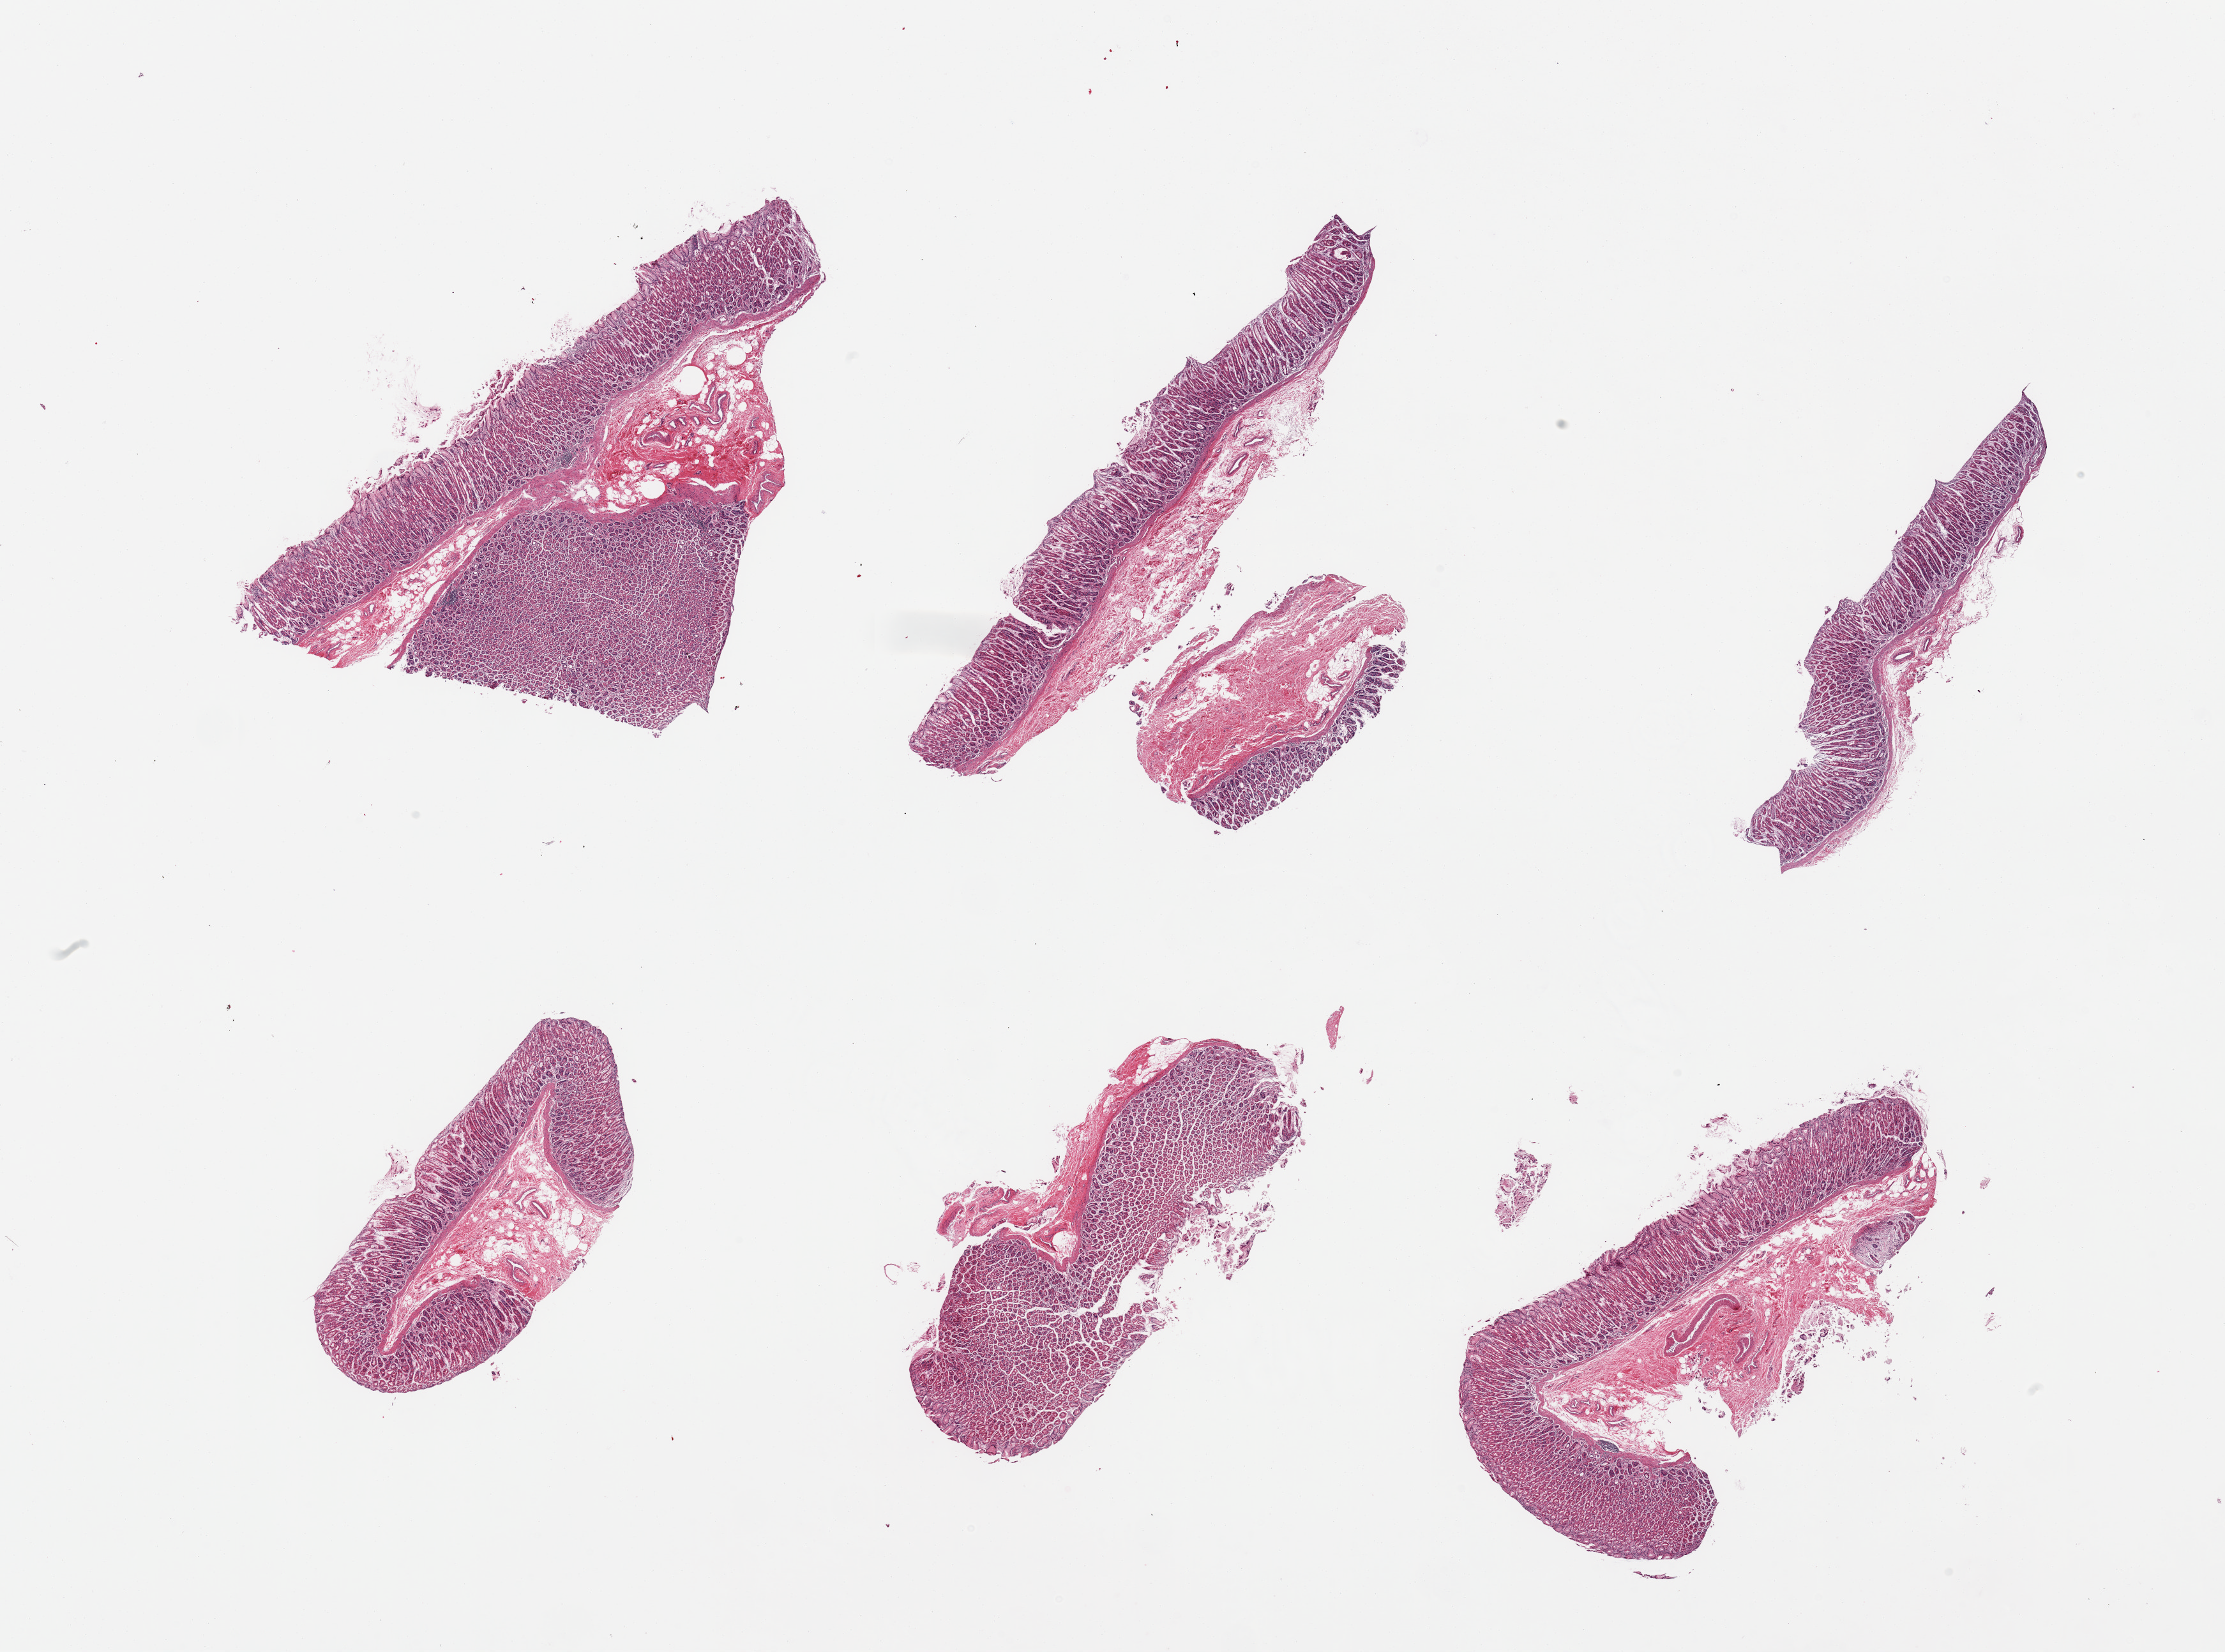
Digitized hematoxylin and eosin (H&E)-stained section, low-resolution overview of the scanned area, about 27.6 x 20.5 mm (acquisition: 20x scan). PAXgene-fixed, paraffin-embedded tissue. Sampled site (target tissue): stomach. Donor tissue sample. Donor sex: male.
Reviewer comment on this tissue sample: 6 pieces; mucosa only present; muscularis missing.